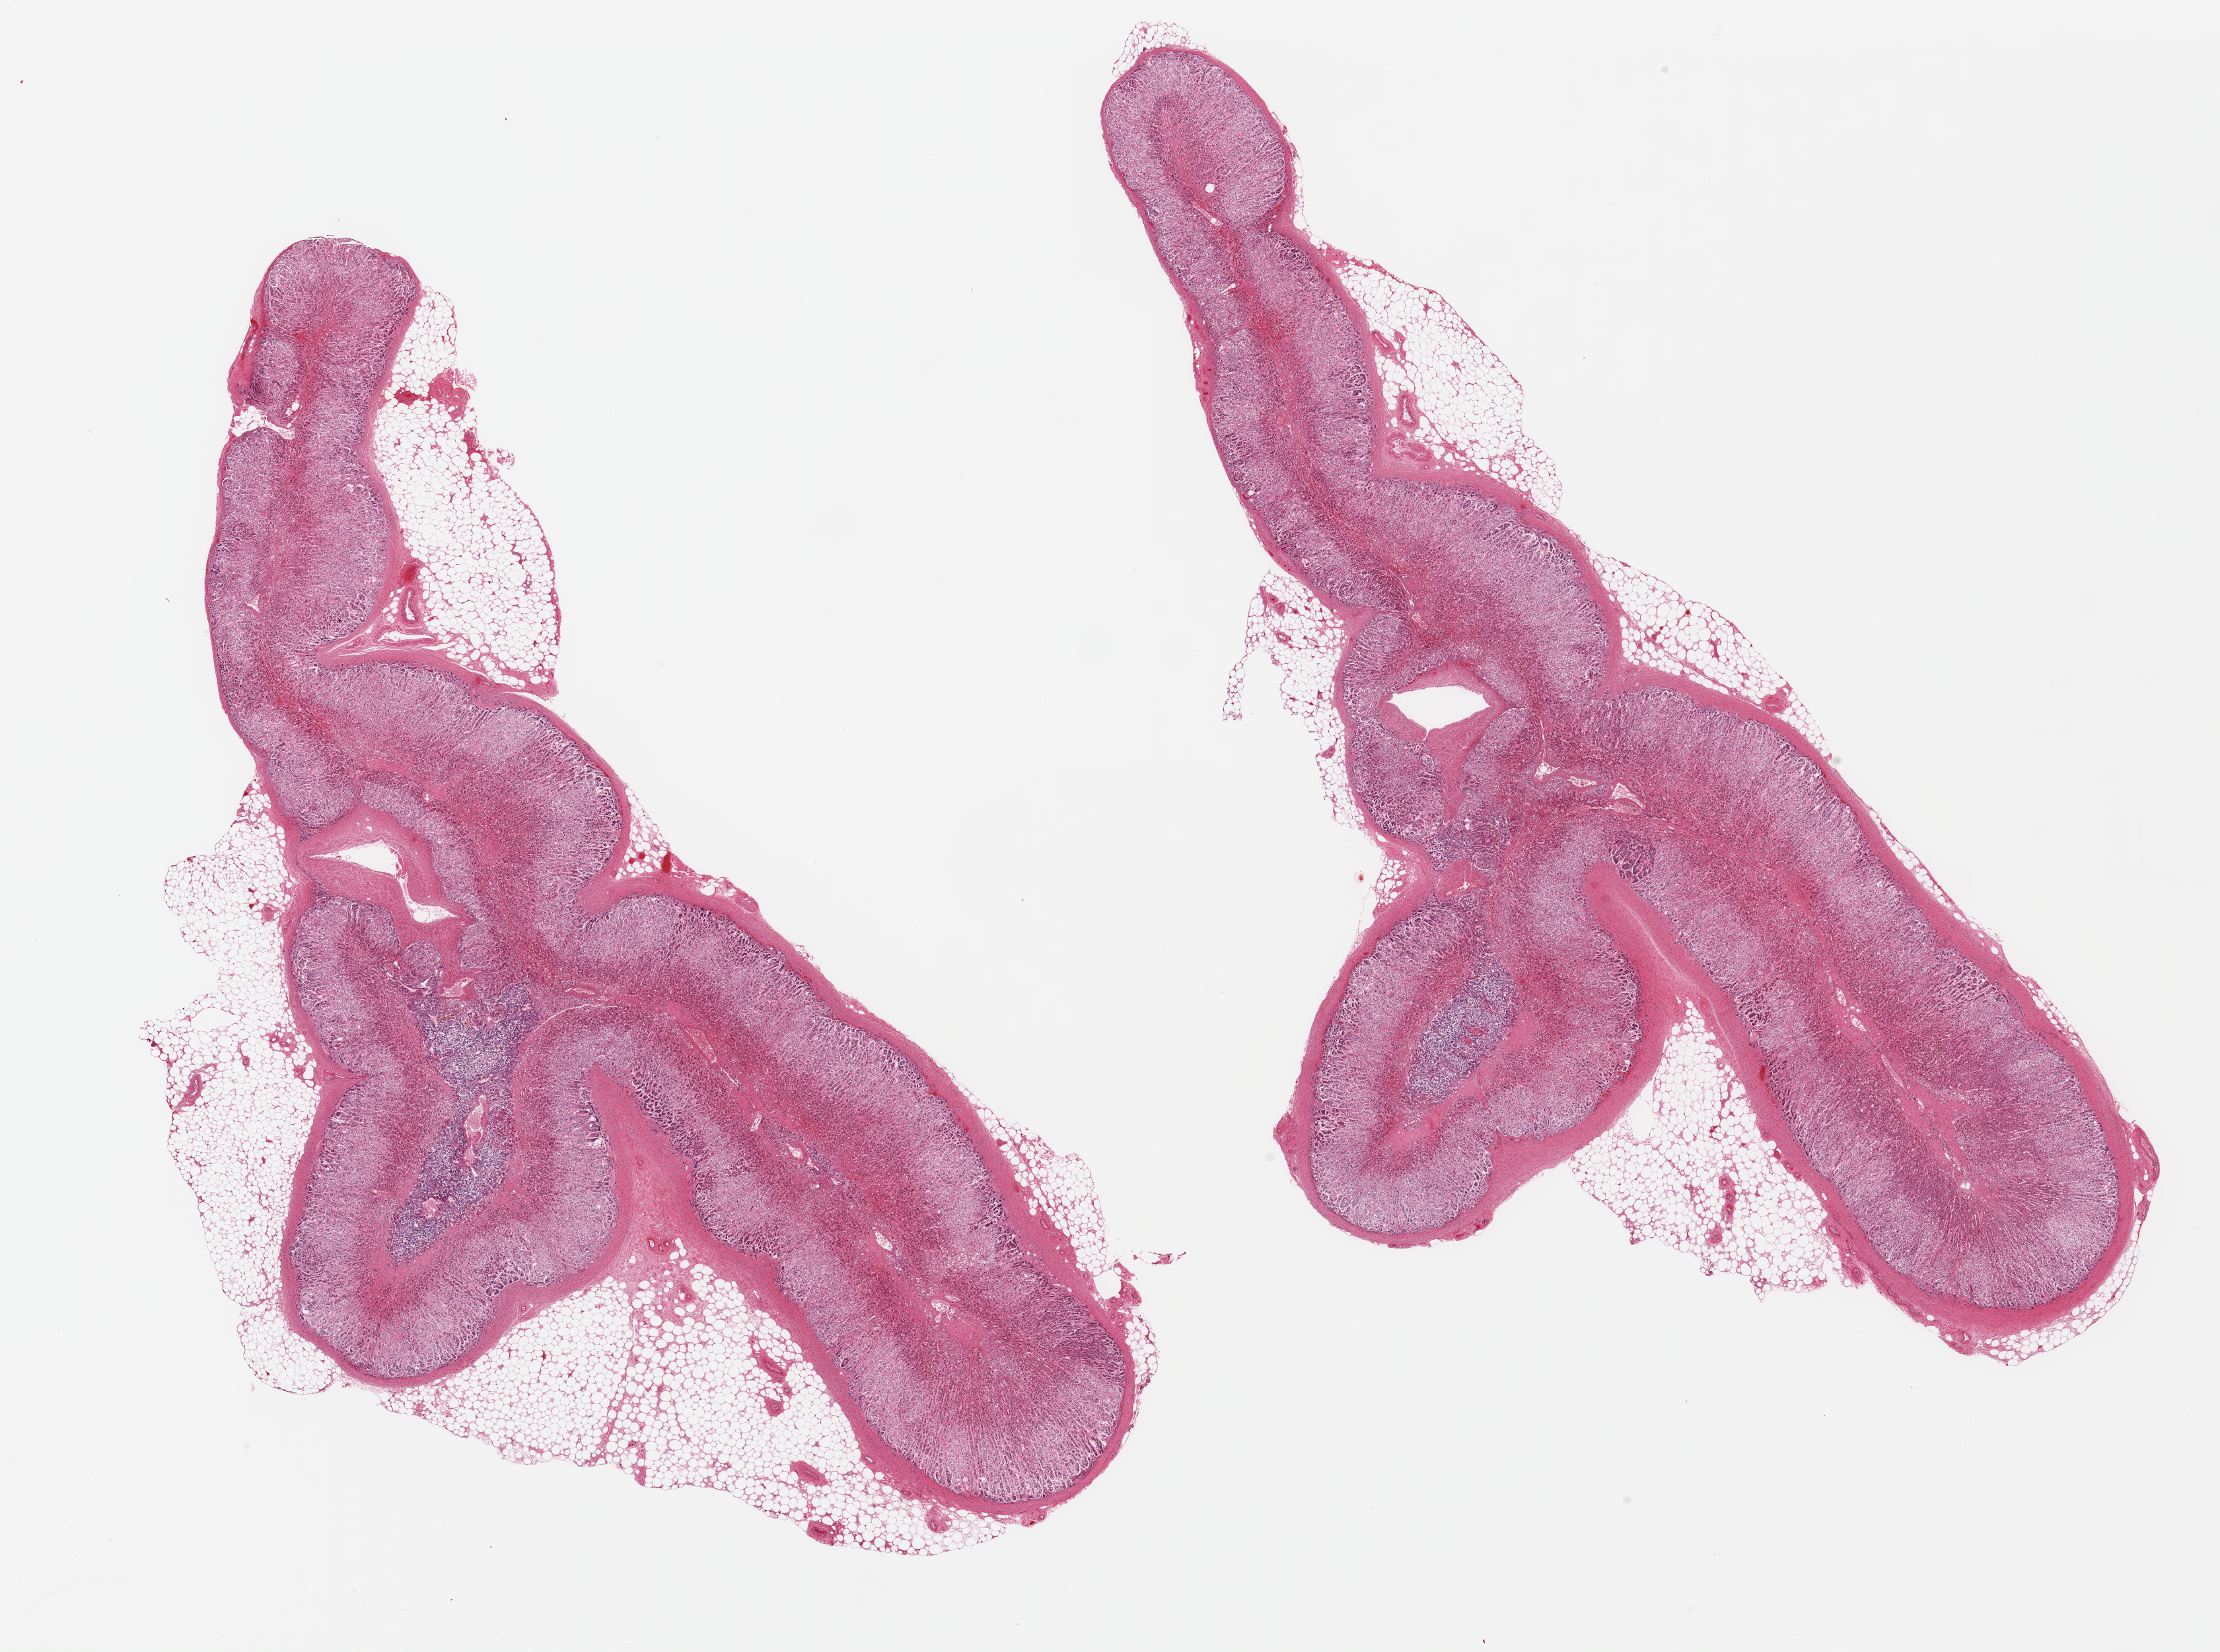
H&E whole-slide image, a low-resolution overview of the entire scanned area, about 26.6 x 19.8 mm, PAXgene-fixed, paraffin-embedded tissue, target tissue: adrenal gland, donor tissue sample.
• pathologist's review note for this sample: 2 pieces, mainly cortex, ~3.5mm focus of medulla; rim of adherent fat up to 2.5mm